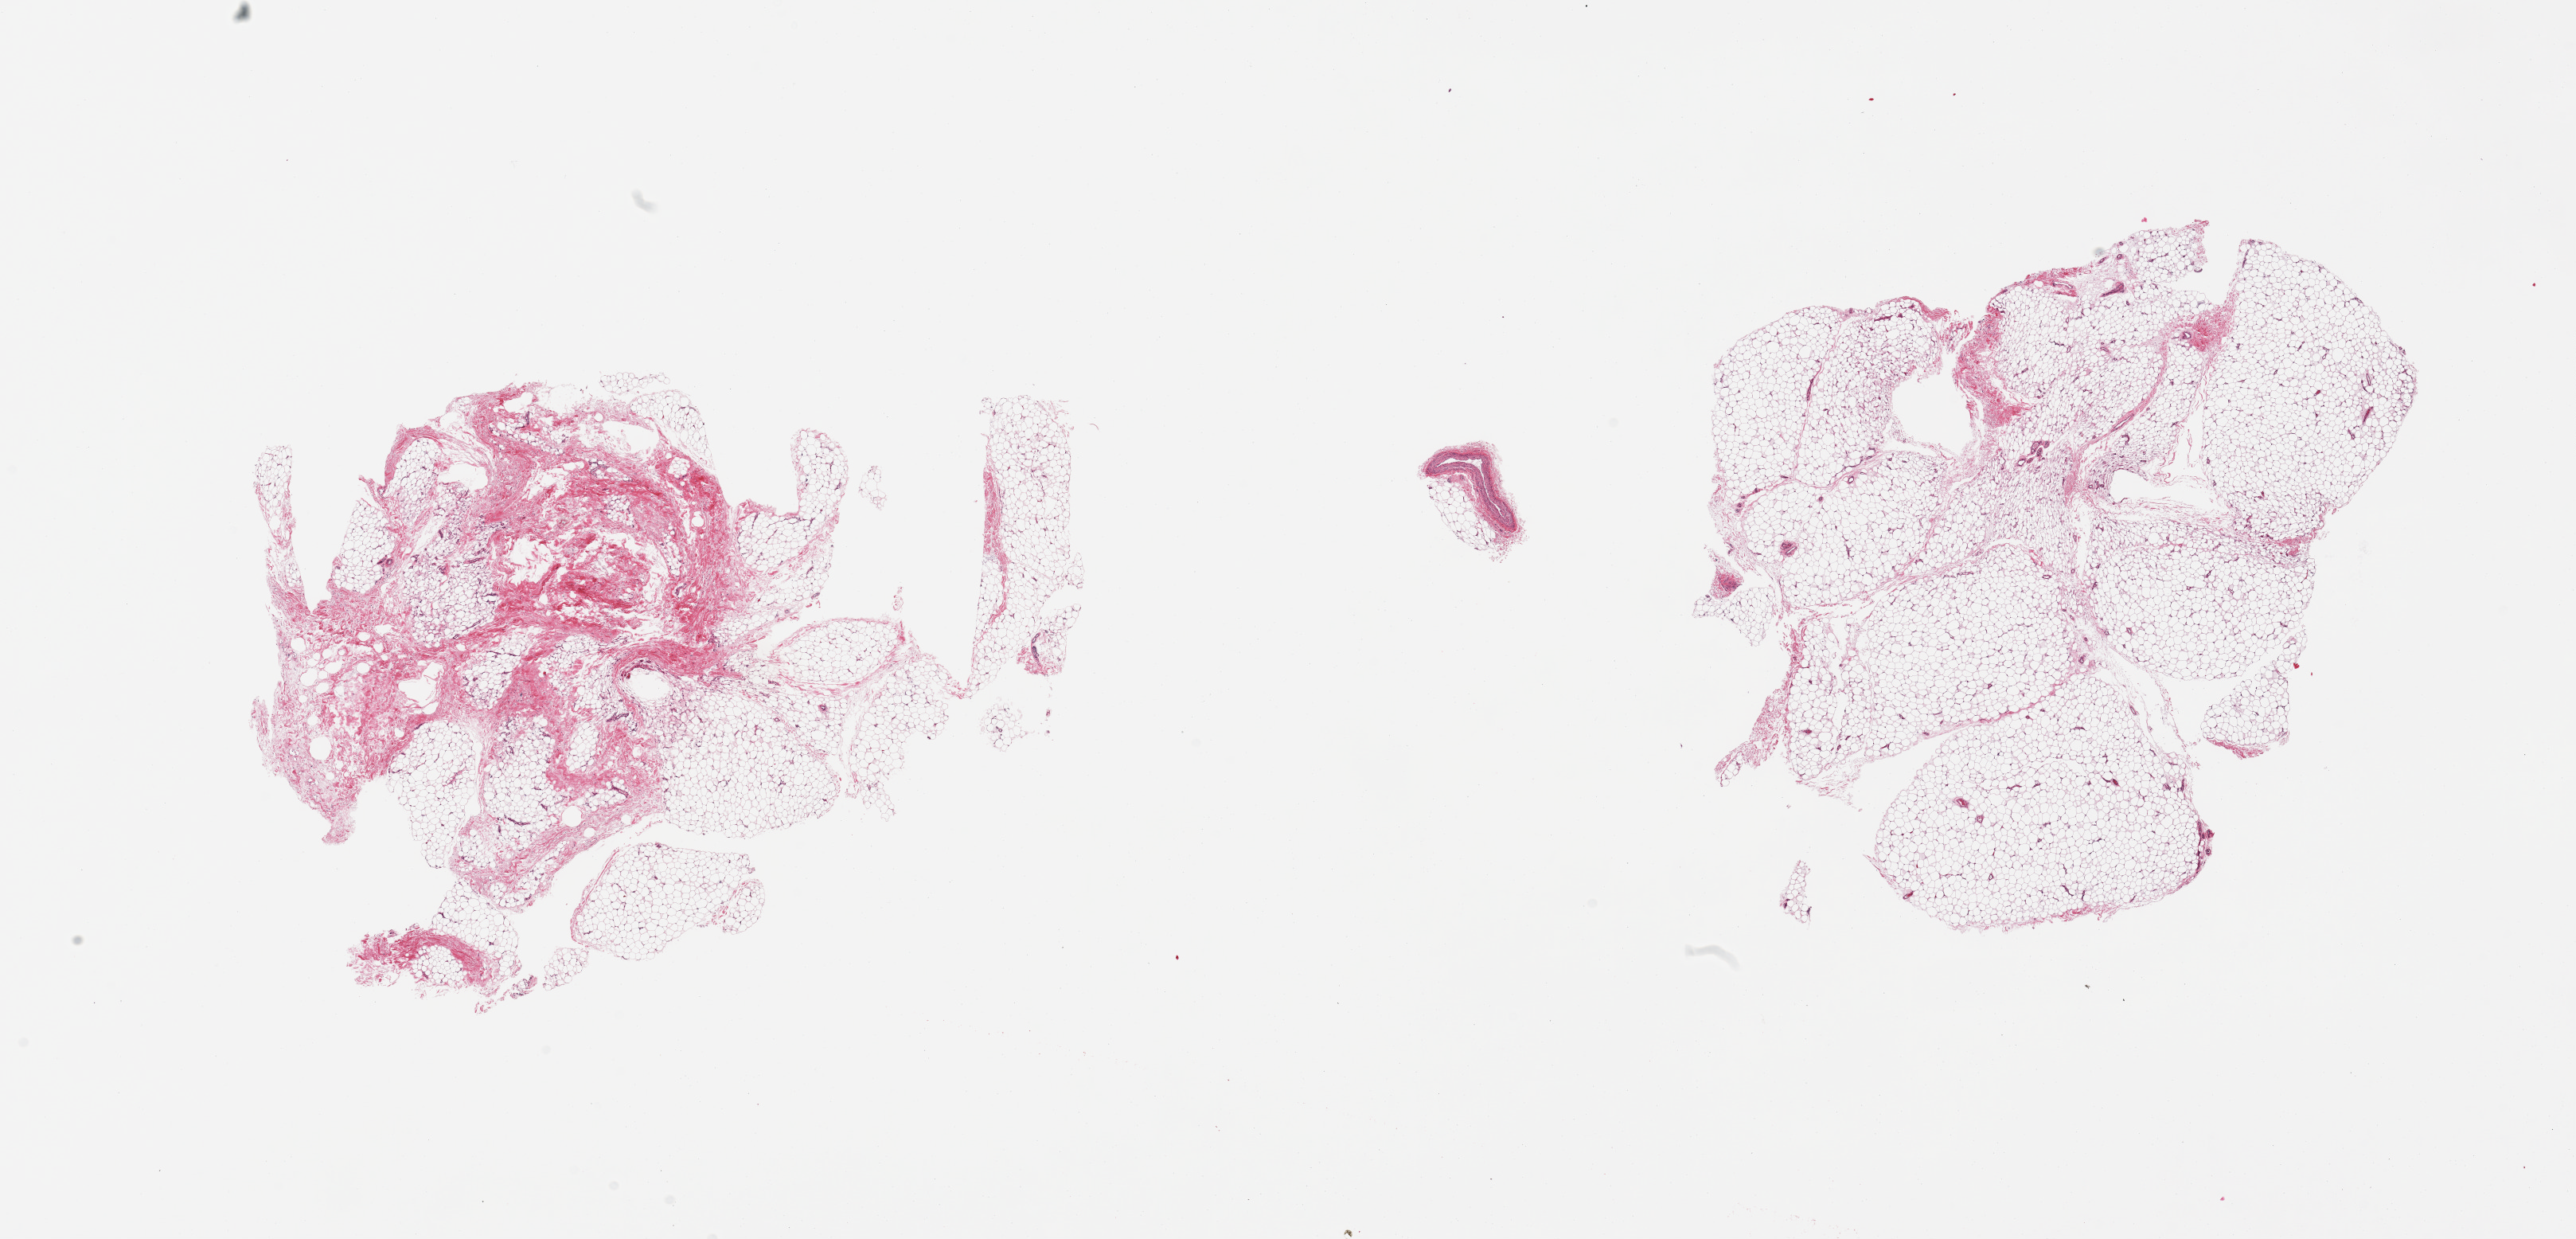
Hematoxylin and eosin (H&E) whole-slide image, low-resolution overview of the scanned area, about 25.6 x 12.3 mm (acquisition: 20x scan), PAXgene-fixed, paraffin-embedded tissue, section of adipose tissue (target tissue), donor tissue sample. Female donor.
- reviewer comment on this tissue sample: 2 pieces; 1 with 30% fibrous content